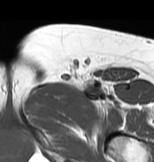
MRI of an extremity soft-tissue mass, one axial slice; position 51 of 83 along the scan axis; MR volume resampled by the dataset authors to the PET/CT grid (not the native acquisition matrix); 3.27 mm slice thickness; 154 × 162 image matrix, field of view 150 × 158 mm. Female patient. From the clinical record (not read from this slice): histological type: myxofibrosarcoma; grade: intermediate; site of the primary tumour: left thigh.
Structures marked on this image (expert contour drawn on MRI and transferred to this co-registered scan by the dataset authors):
- gross tumour volume including surrounding oedema: bounding box <30,77,118,115> (left, top, right, bottom; pixels)